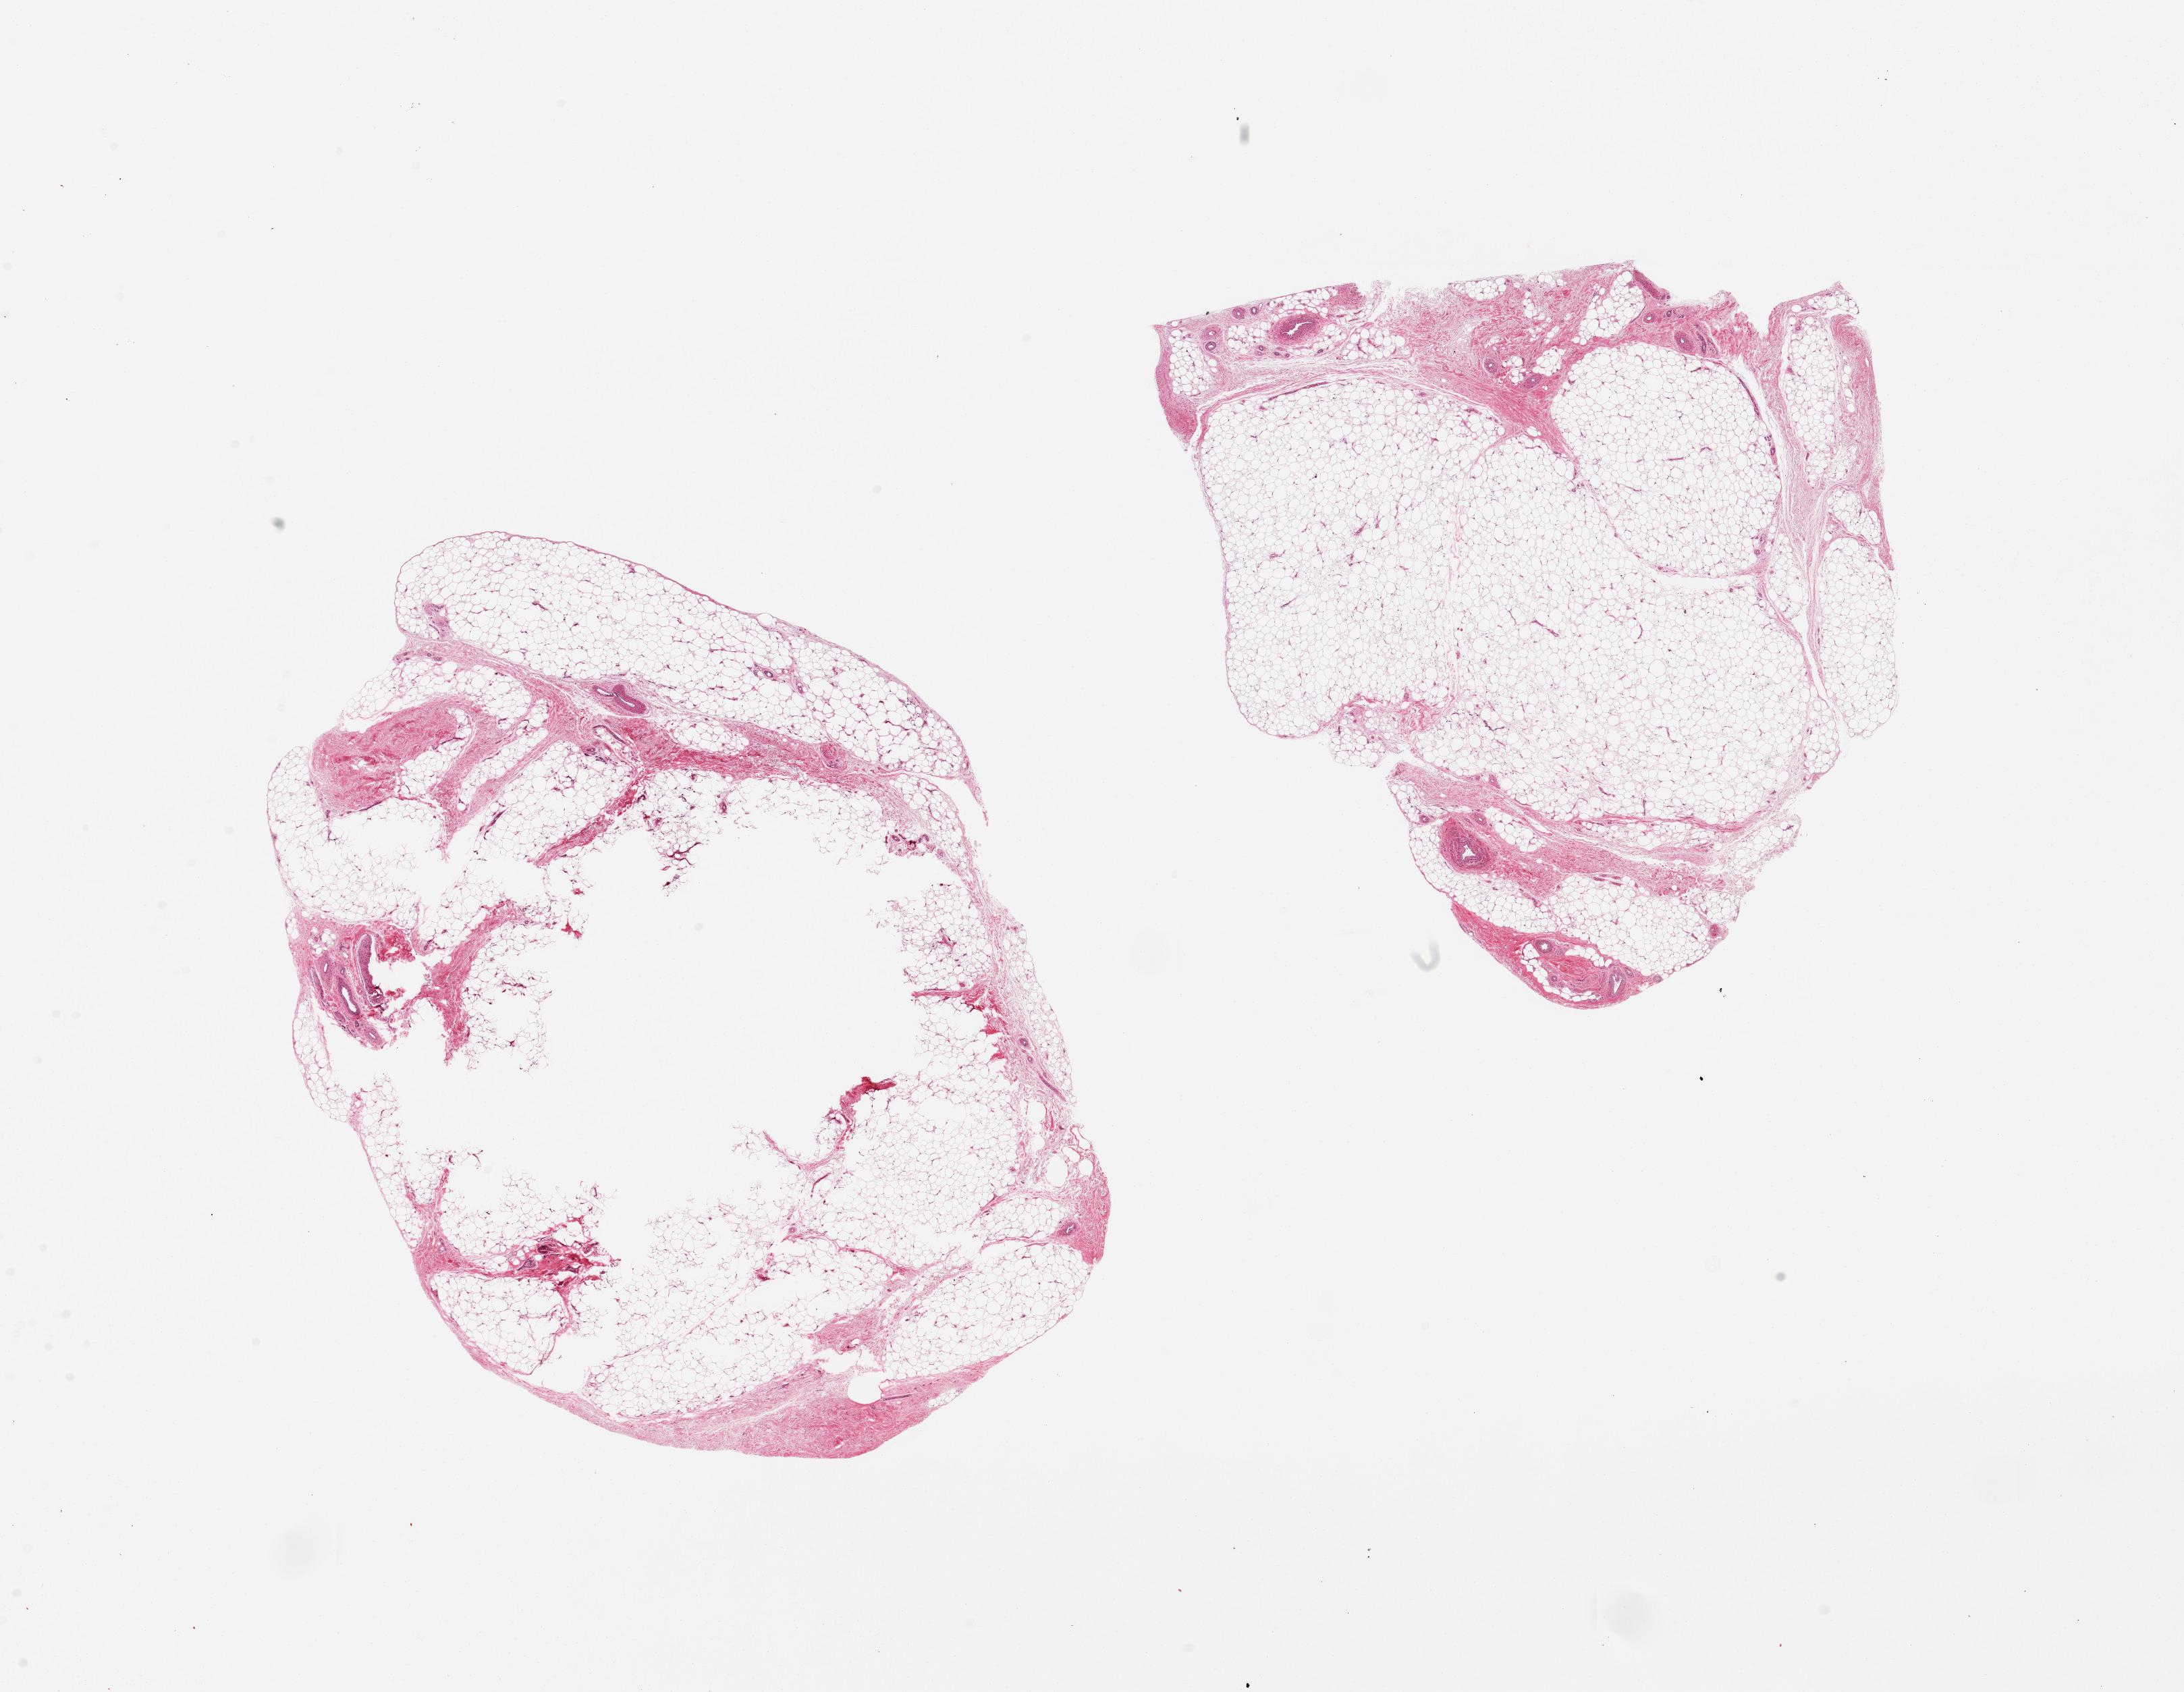
Whole-slide image, hematoxylin and eosin (H&E) stain, low-resolution overview of the scanned area, about 25.6 x 19.8 mm; PAXgene-fixed paraffin-embedded (PFPE) section; sampled site (target tissue): adipose tissue; donor tissue sample. Donor: male.
Pathologist's review note for this sample: 2 pieces, 12x9 & 9x8mm; ~10-15% fibrous tissue.